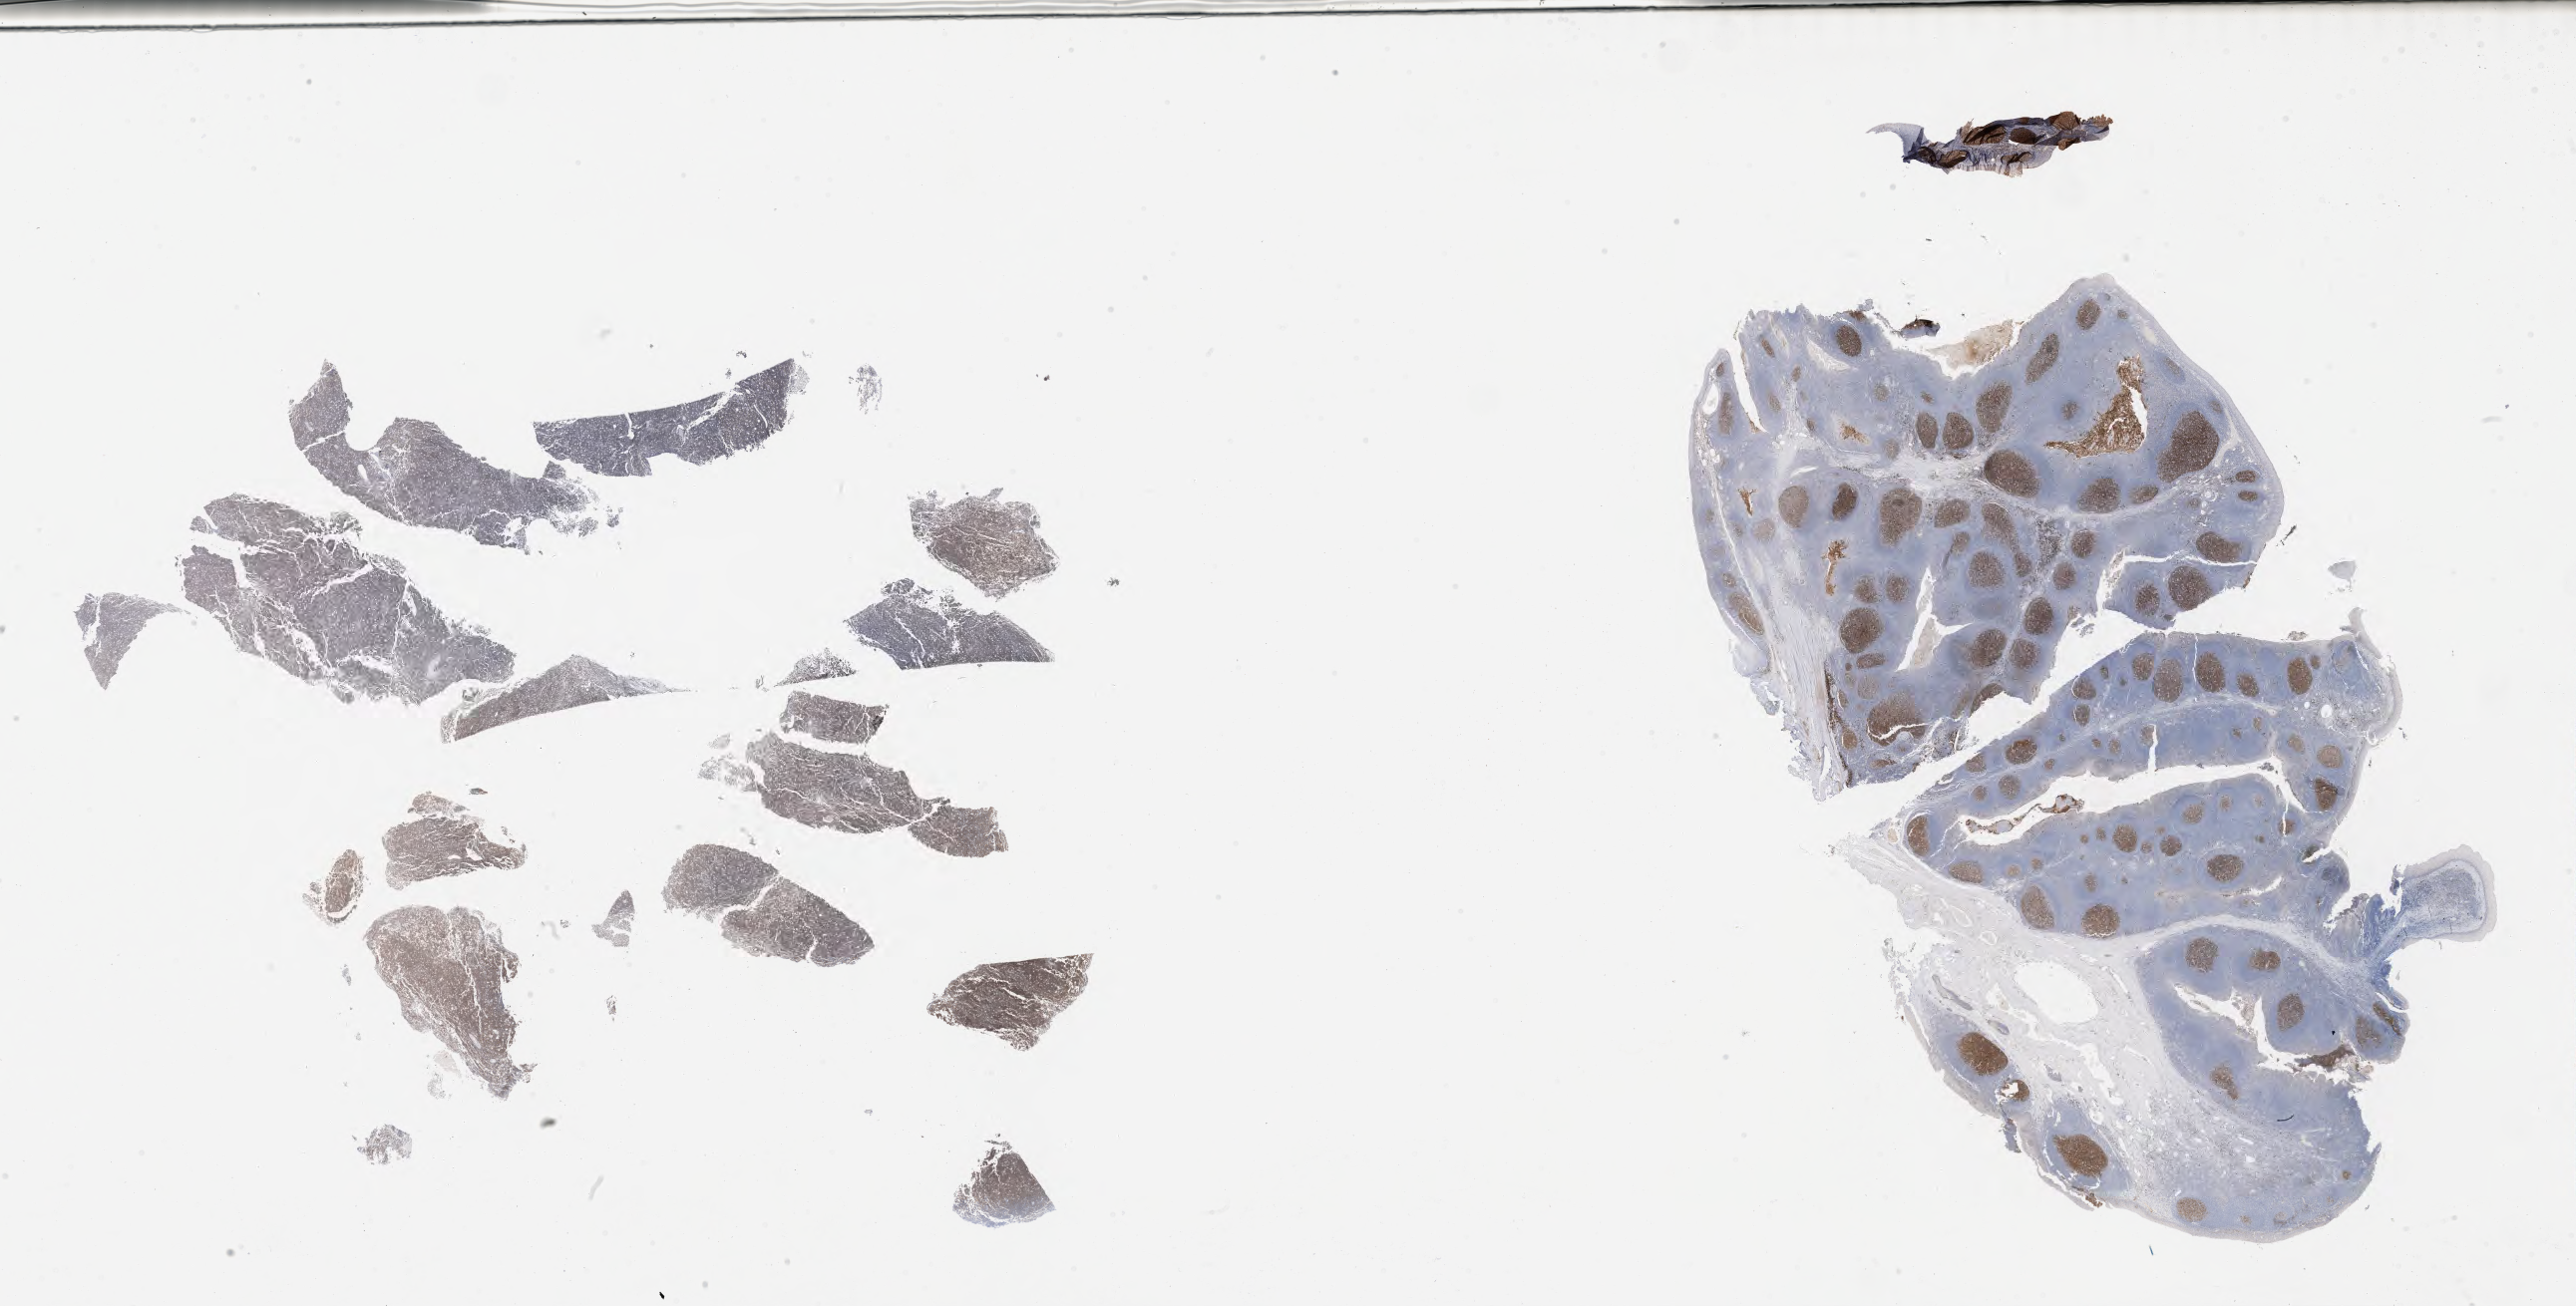
IHC for CD10, whole-slide image — shown as a low-resolution overview of the whole scanned area (about 41.7 x 21.2 mm); specimen: tumor tissue. Patient: male, age 11 years.
Diagnosis: Burkitt lymphoma, NOS.